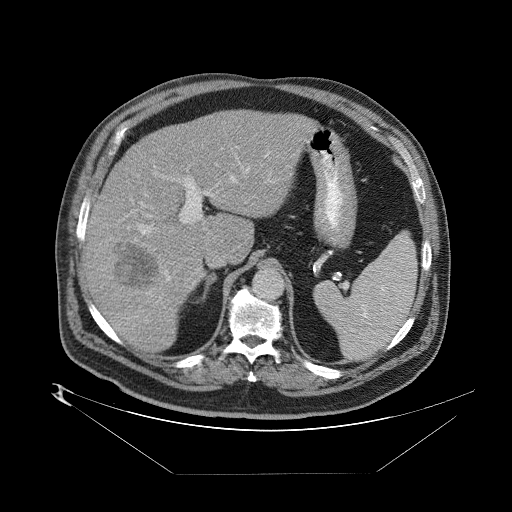
Contrast-enhanced abdominal CT (liver protocol), one axial slice. Position 54 of 89 along the scan axis. 140 kVp. One of 2 acquisitions stored at this slice position. Soft-tissue window (W 400 / L 40 HU). 512 × 512 image matrix, field of view 480 × 480 mm. From the clinical record (not read from this slice): diagnosis: hepatocellular carcinoma (patient treated with transarterial chemoembolisation; whether this scan precedes or follows treatment is not stated here); TNM stage (as recorded): Stage-II; Child-Pugh class: B; tumour differentiation: moderately differentiated; tumour nodularity: multinodular.
Structures marked on this image (semi-automatic segmentation, software-assisted and operator-edited):
- abdominal aorta: box from (x=253, y=267) to (x=284, y=299) px
- liver parenchyma outside the tumour (the mass and vessels are separate outlines, so this box may not span the whole liver): (x=82, y=106)–(x=310, y=352)
- mass: (x=112, y=242)–(x=160, y=288)
- liver vessels: (x=88, y=151)–(x=269, y=341)